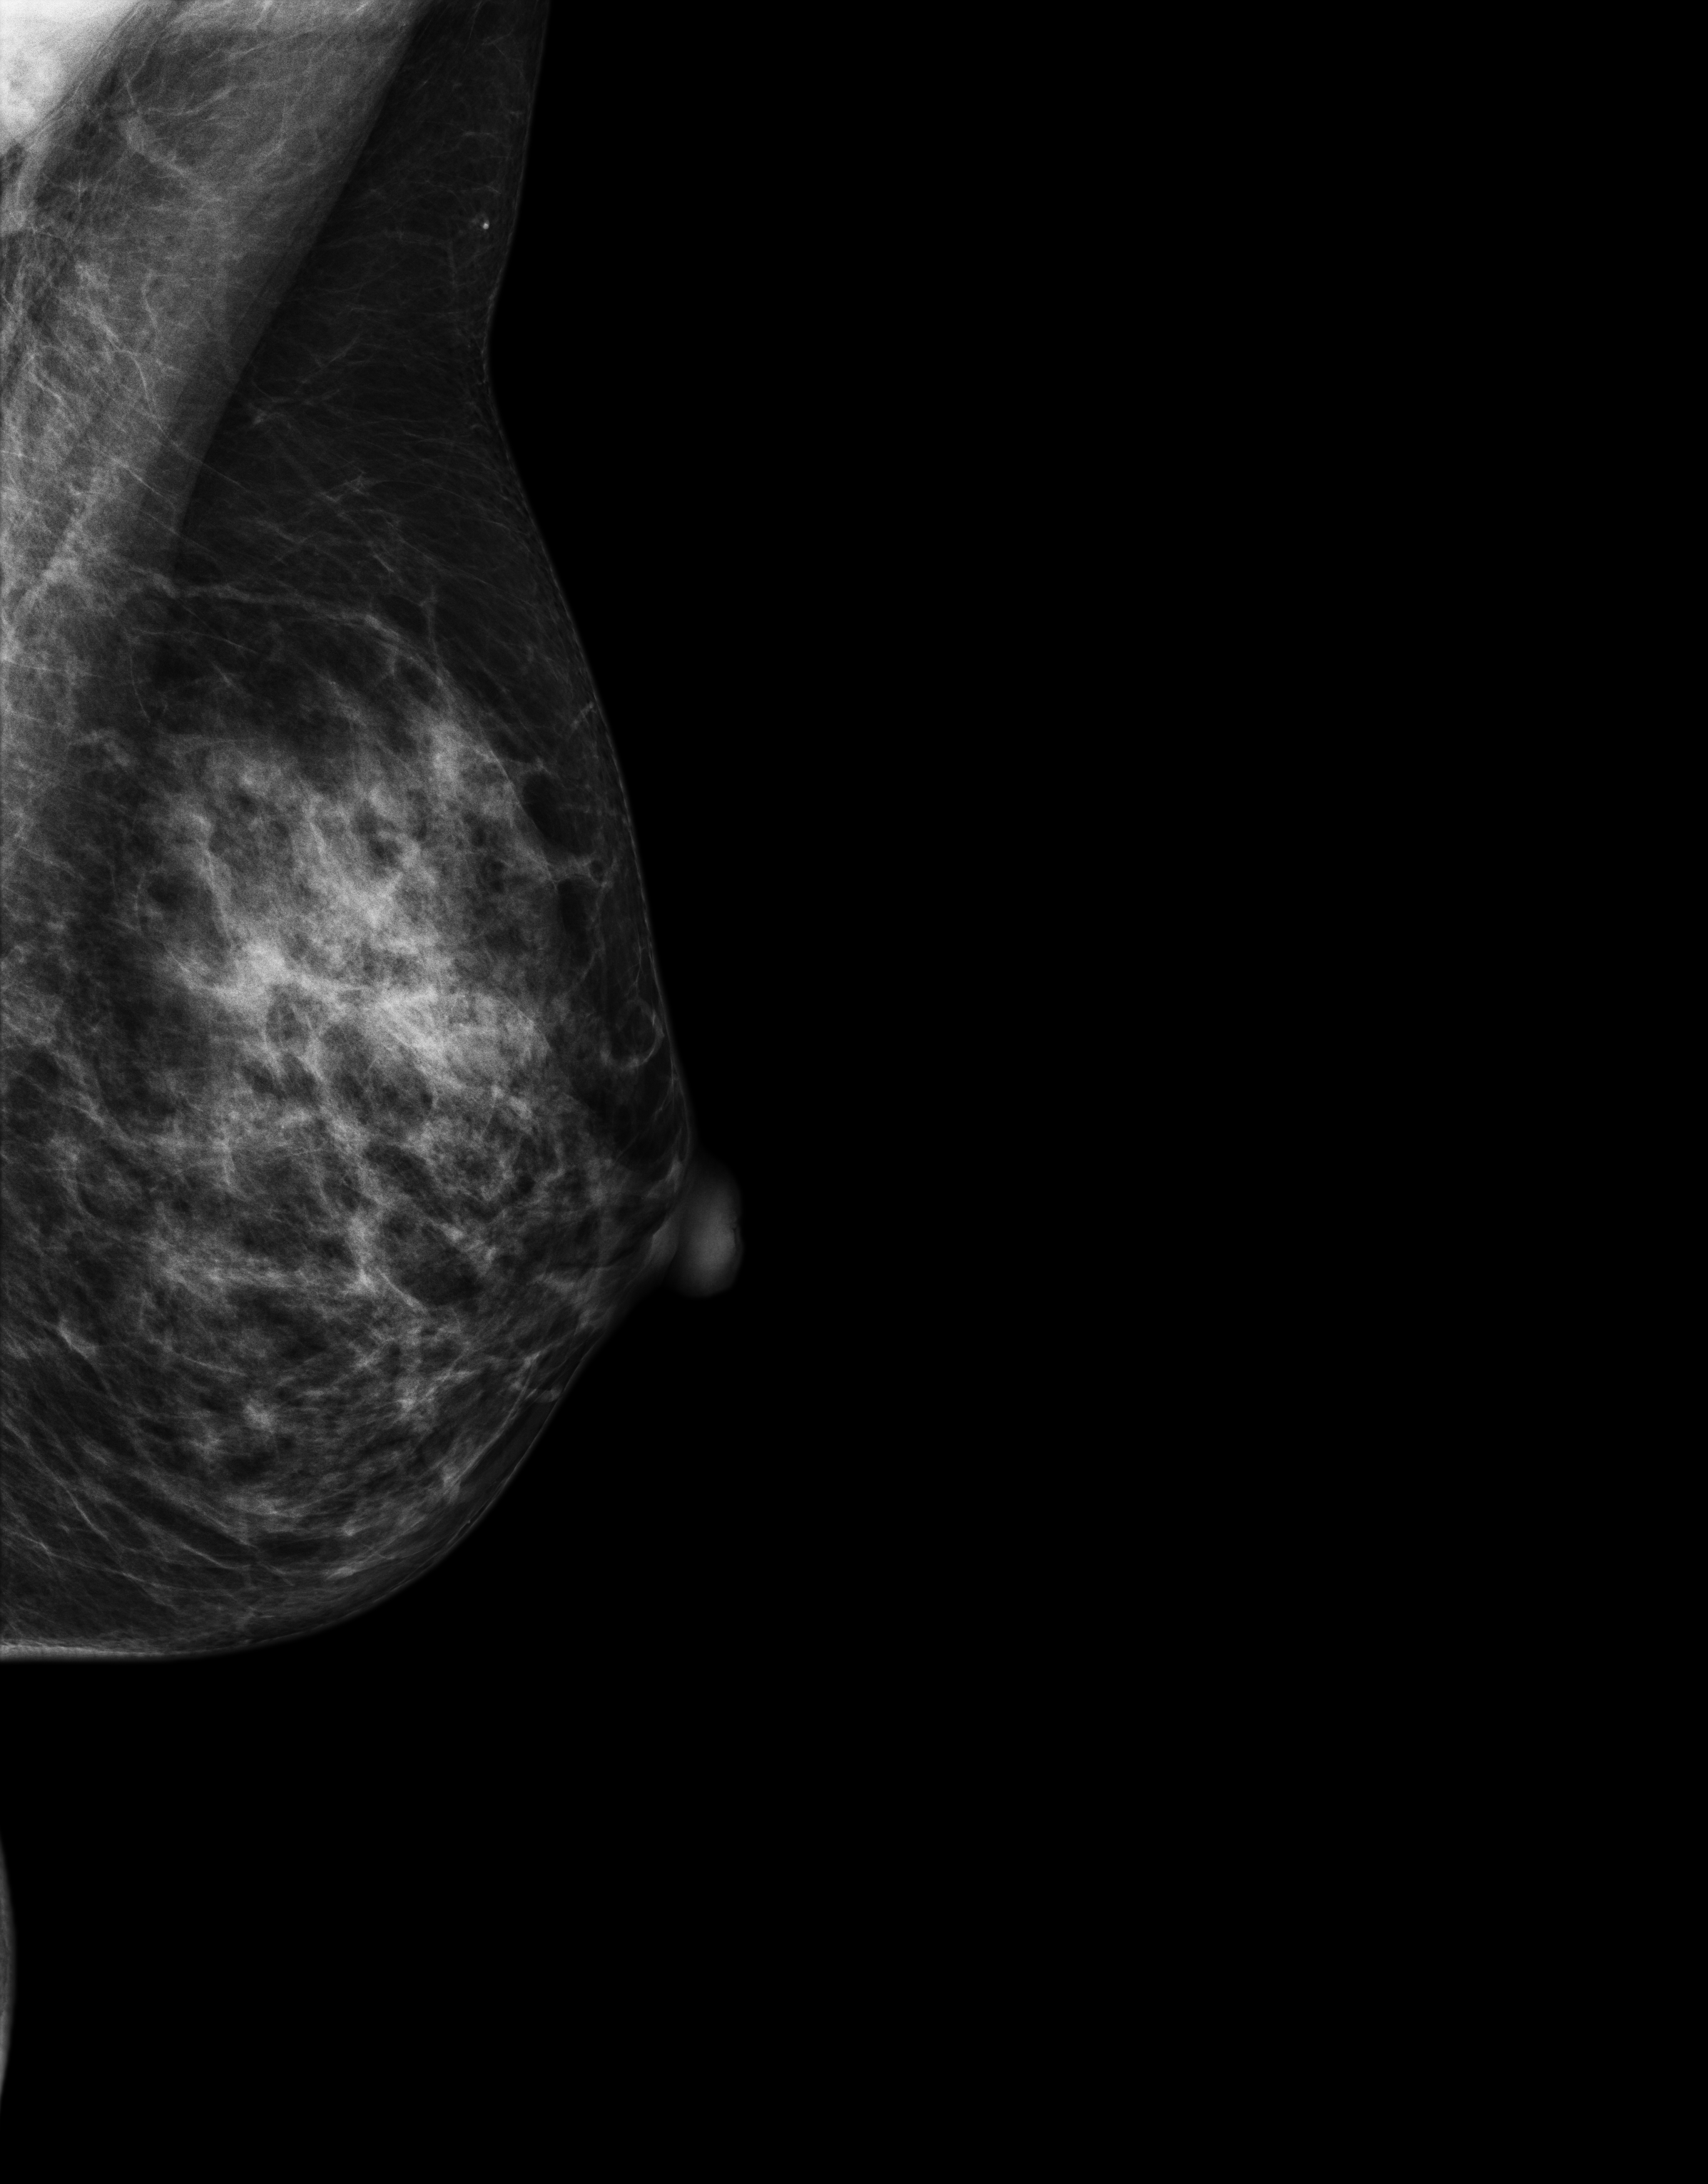
Digital mammogram (FFDM); left breast; medio-lateral oblique projection; annual screening mammography examination. Patient: female, 42 years.
BI-RADS breast density category at the screening exam (both breasts, scale 1–4): 4. Final BI-RADS category for the screening round (tomosynthesis exam, both breasts): category 1. Recall: no recall after this screen.